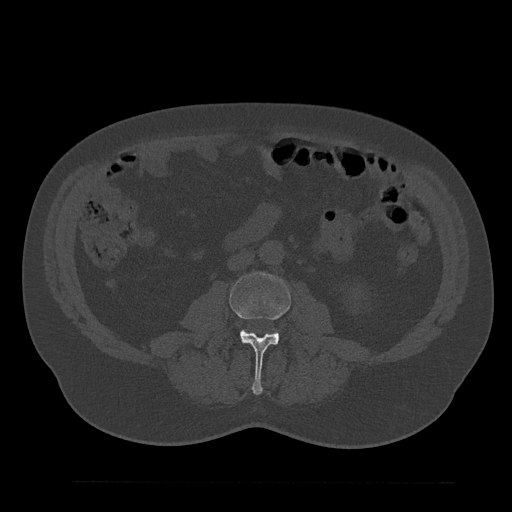
CT including the spine, one axial slice. Slice 21 of 797 in the series (ordered by position). 120 kVp. Bone window (W 1800 / L 400 HU). 0.5 mm slice thickness. 512 × 512 image matrix, field of view 430 × 430 mm. Male patient, age 61 years. Case-level facts recorded for this patient, not image findings: primary cancer: prostate.
Structures marked on this image (semi-automatic segmentation, software-assisted and operator-edited):
- L3 vertebra: bounding box [x1, y1, x2, y2] px = [229, 273, 291, 395]